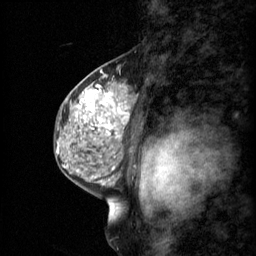
Breast MRI (dynamic contrast-enhanced), one sagittal slice. Position 39 of 60 along the scan axis. 3 images stored at this slice position (order not interpretable as contrast timing). 1.5 T. TE 4.2 ms, TR 11 ms. 256 × 256 image matrix, field of view 200 × 200 mm. Female patient, age 48 years.
Outlined on this slice (semi-automatic segmentation, software-assisted and operator-edited):
- analysis volume of interest (the breast-tissue region the enhancement analysis was run in; not a lesion): box from (x=69, y=74) to (x=134, y=147) px
- tumour enhancement mask (voxels above the 70 % enhancement threshold inside the analysis volume of interest): (x=78, y=84)–(x=131, y=139)